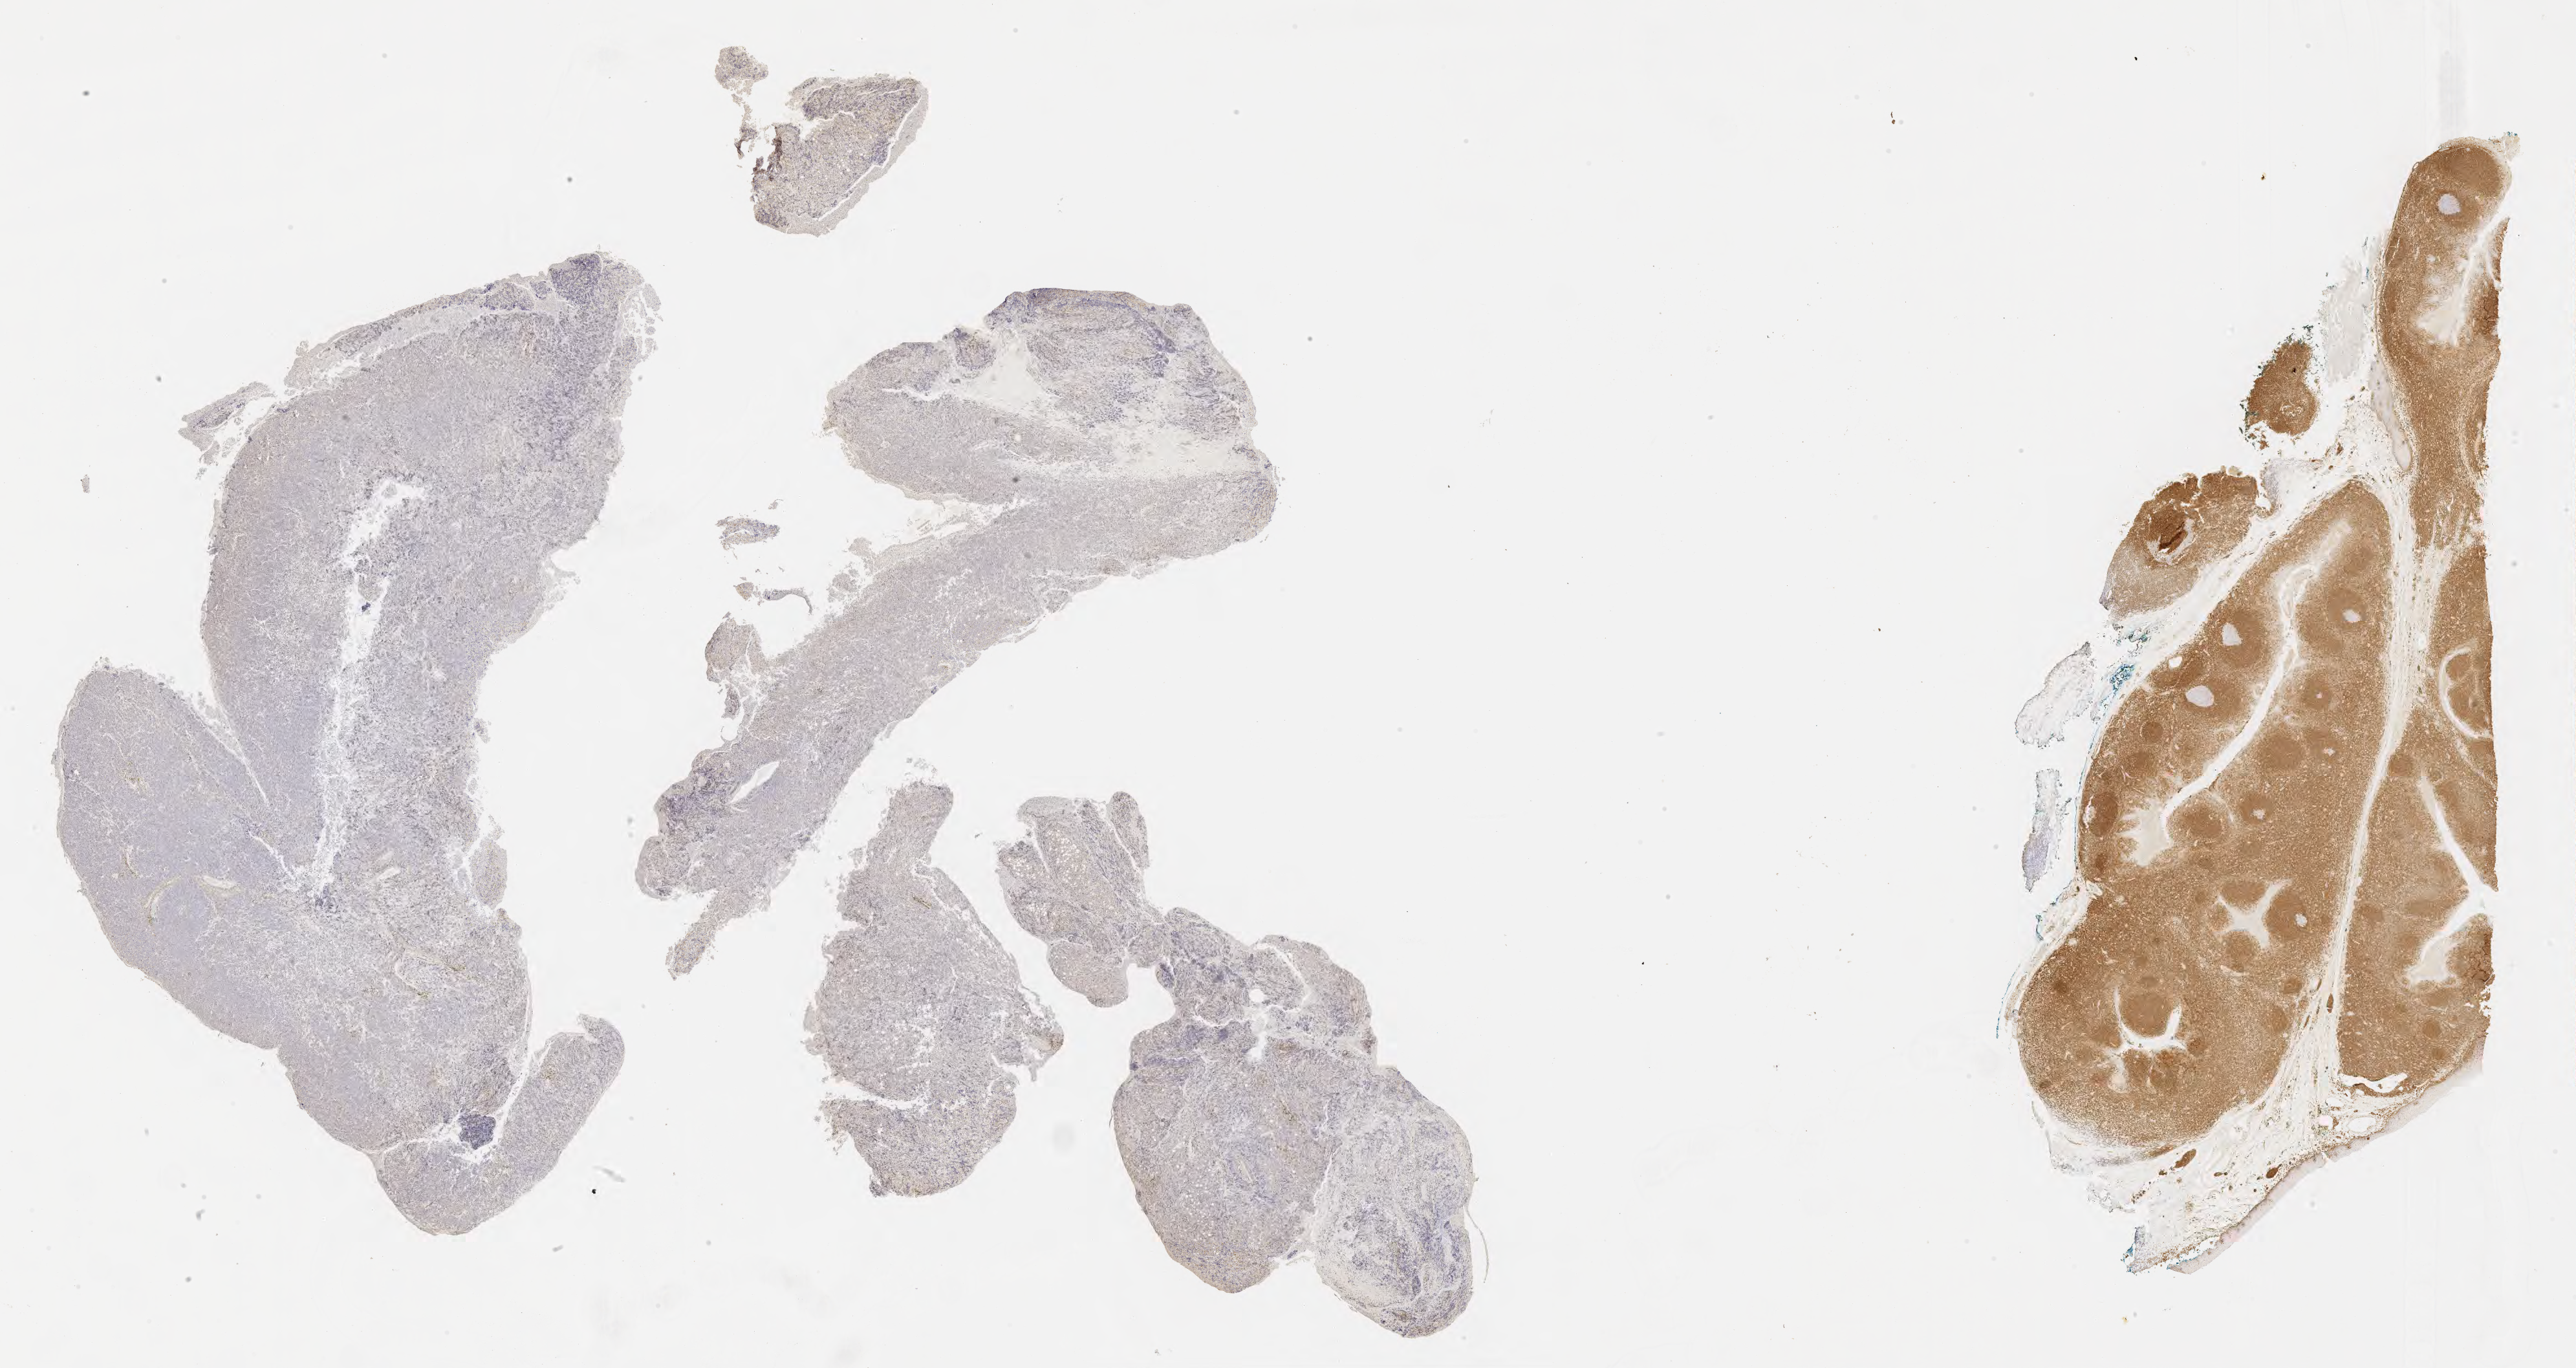
IHC for BCL2, whole-slide image — a low-resolution overview of the entire scanned area, about 32.2 x 17.1 mm; tumor tissue; site: abdomen proper. Patient: male, age at initial diagnosis 5 years.
* diagnosis: Burkitt lymphoma, NOS